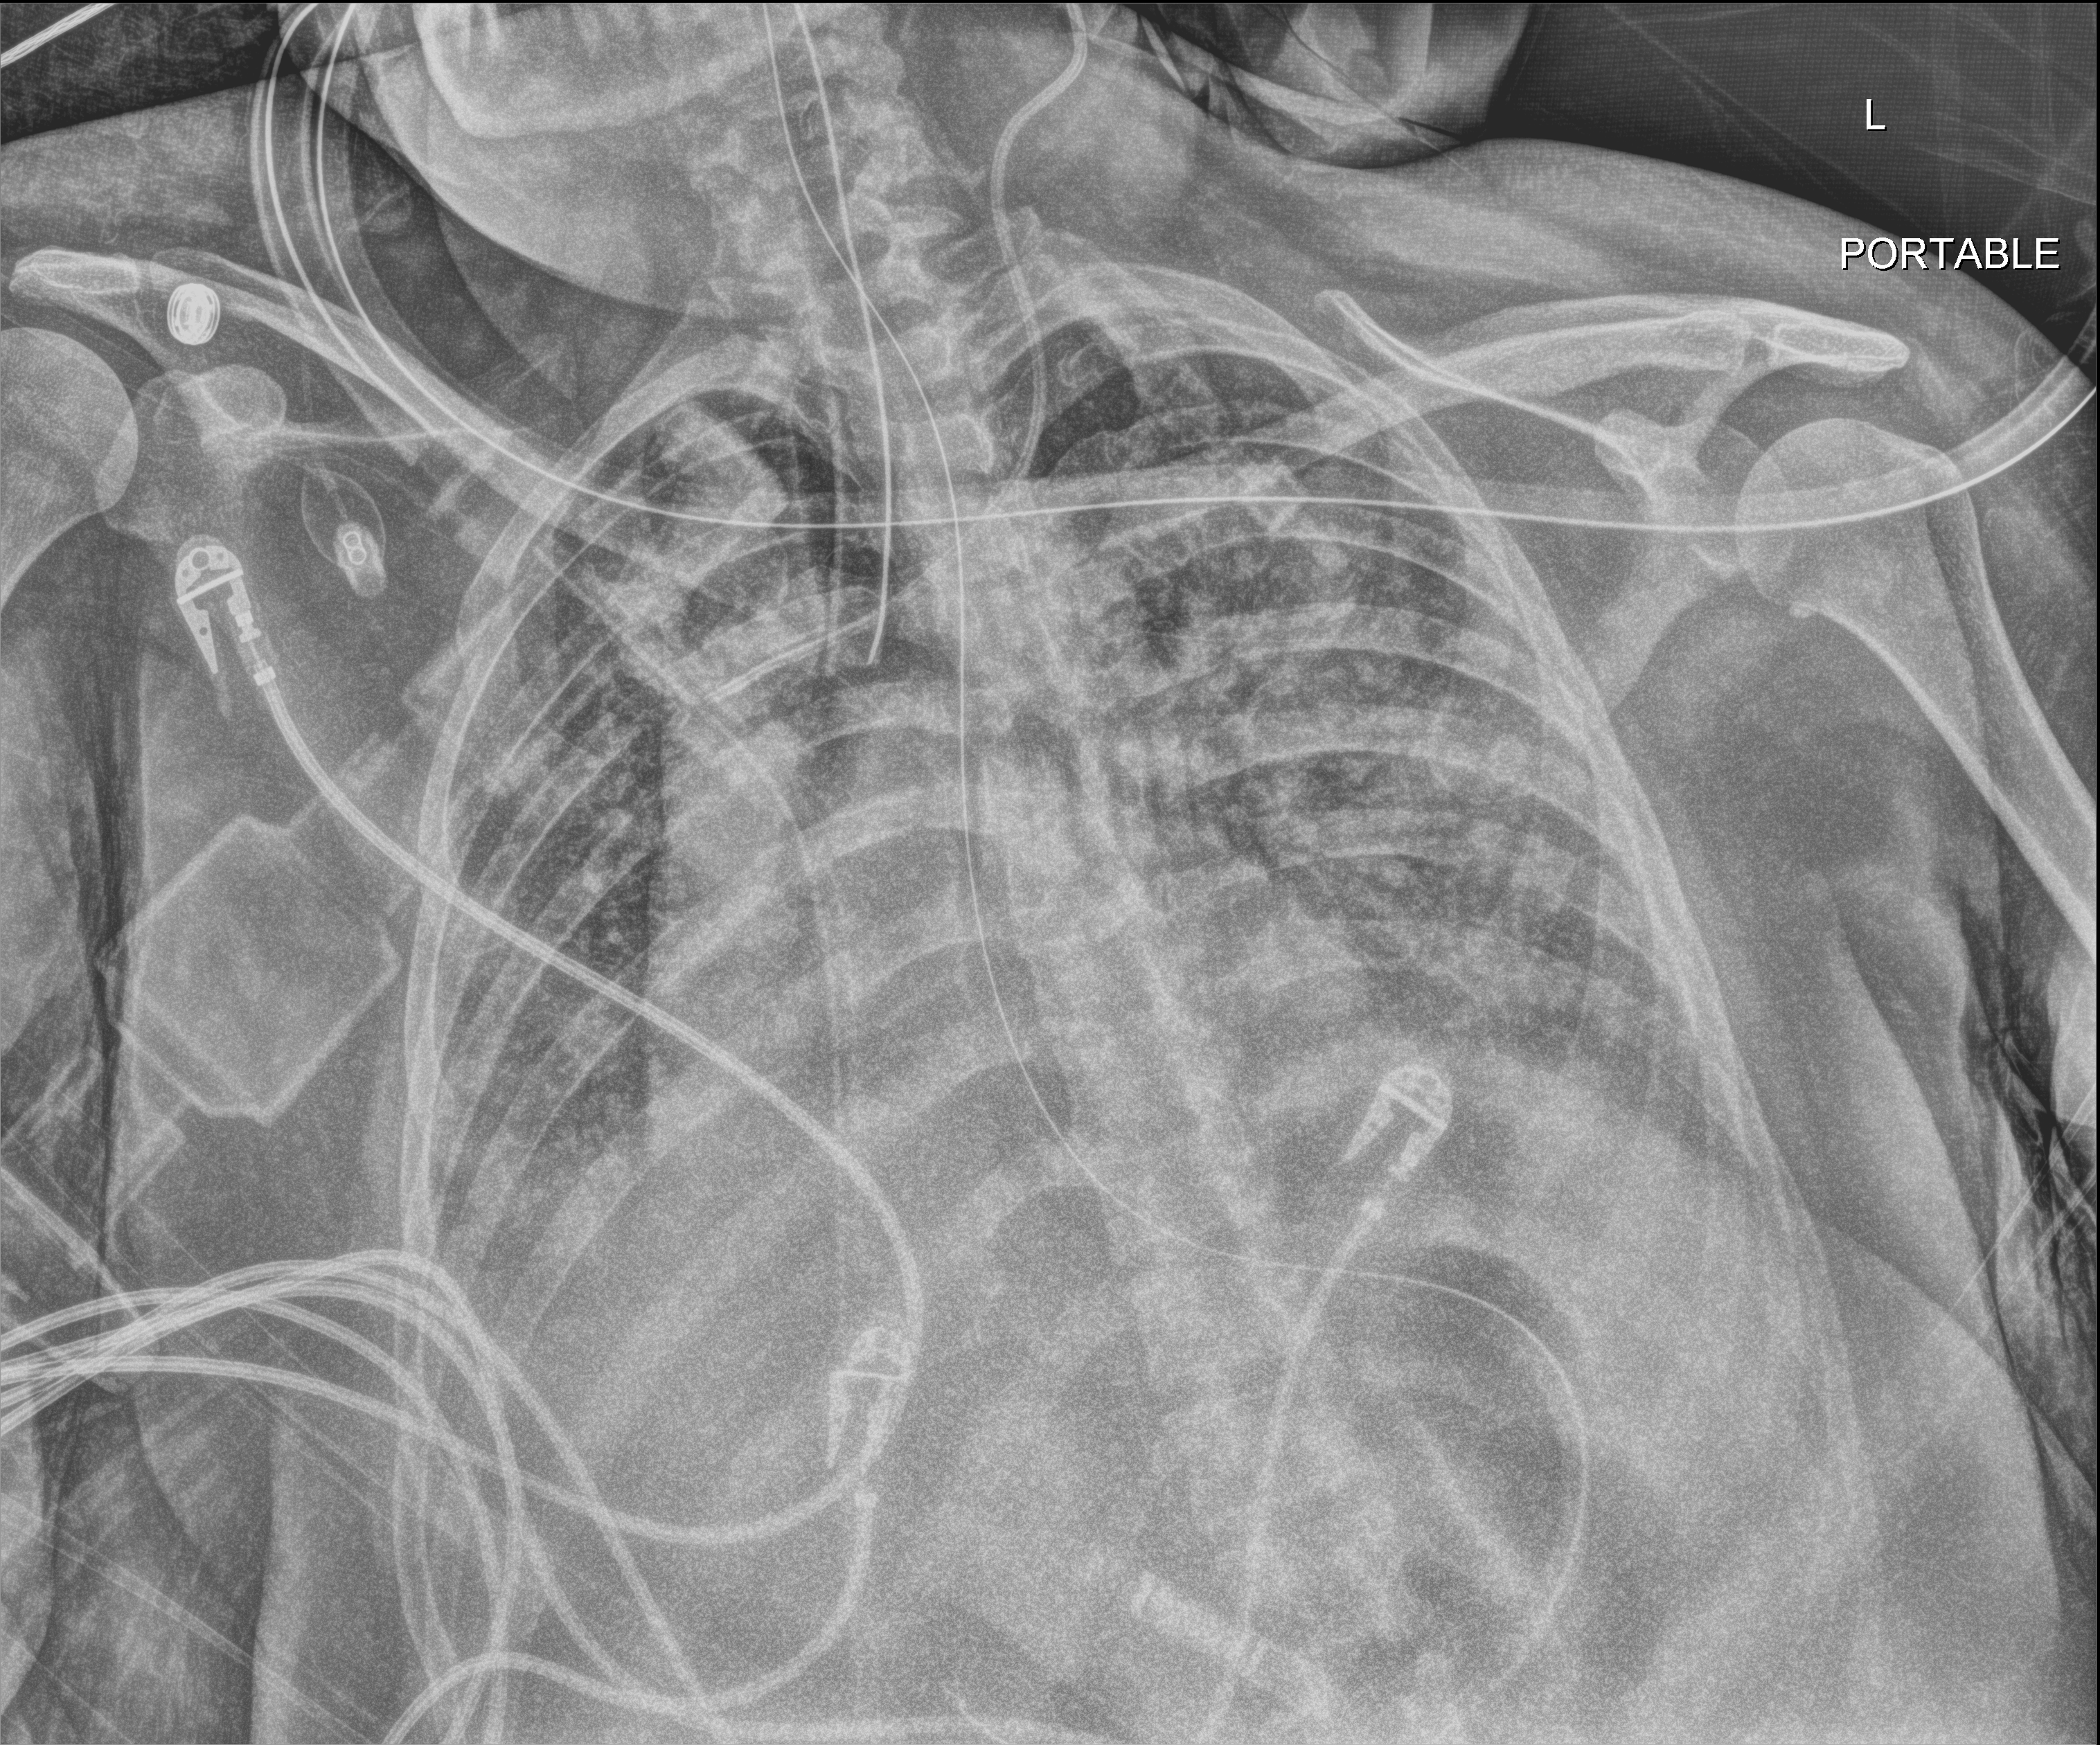
Bedside chest radiograph (digital radiography); anteroposterior (AP) projection. Female patient hospitalised with COVID-19, age 18–59 years.
From the hospital-stay record, not from the radiograph (when in the stay this image was taken is not recorded): mechanically ventilated during this hospital stay: yes; admitted to intensive care during this hospital stay: no.